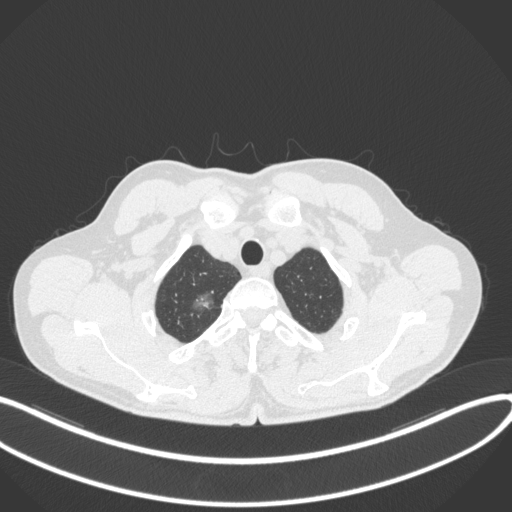
Chest CT, one axial slice; position 344 of 407 along the scan axis; reconstruction kernel B31f; lung window (W 1500 / L -600 HU); 1 mm slice thickness; 512 × 512 image matrix. Patient: male, 58 years. Case-level facts recorded for this patient, not image findings: clinical TNM (as recorded): T1c N0 M0.
Structures marked on this image (bounding box drawn by a radiologist):
- lung tumour (recorded histology: adenocarcinoma): bounding box [x1, y1, x2, y2] px = [190, 289, 219, 314]